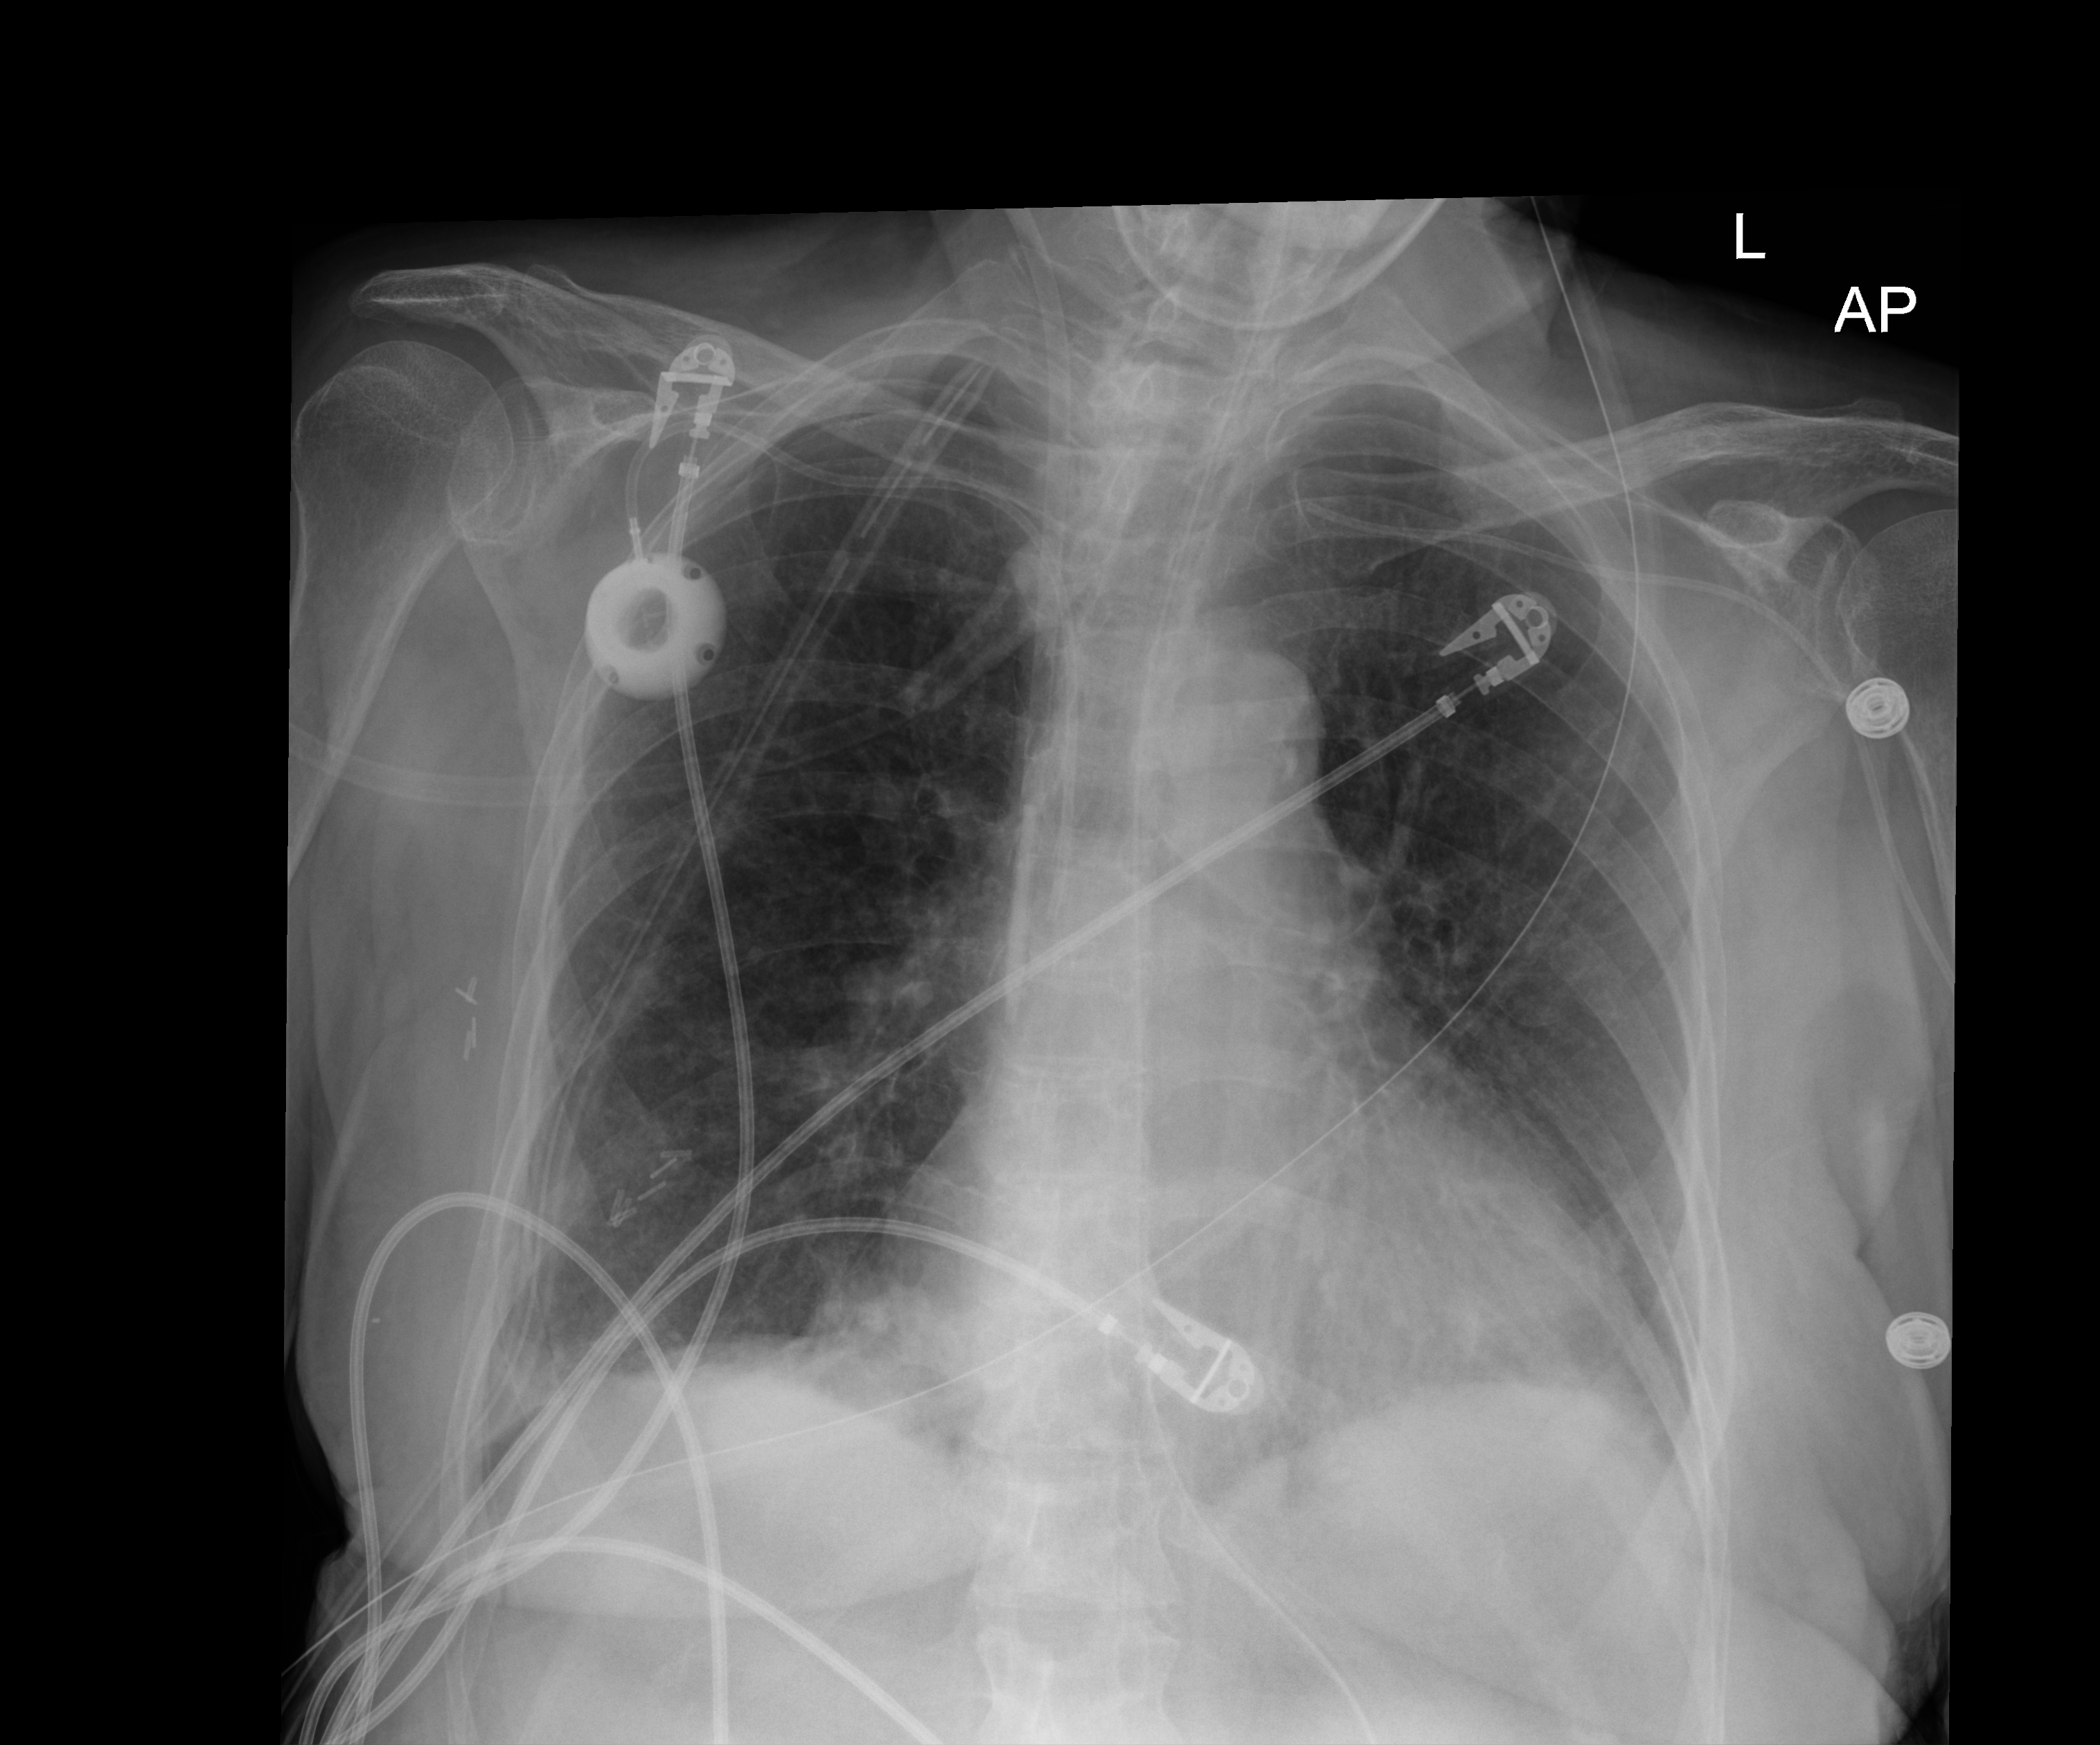
Chest X-ray (portable), anteroposterior (AP) projection. Patient hospitalised with COVID-19; female, aged 60–74 years.
Hospital-stay facts (about this admission, not read from this image; timing relative to this image not recorded):
- mechanically ventilated during this hospital stay: yes